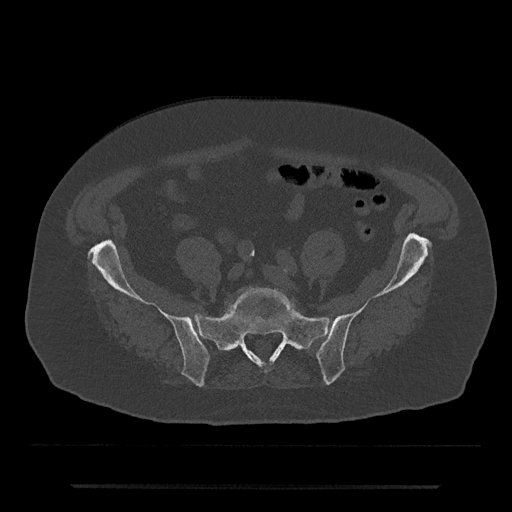
CT including the spine, one axial slice. Slice 246 of 797 in the series (ordered by position). Reconstruction kernel Br40s/3. 120 kVp. Bone window (W 1800 / L 400 HU). 512 × 512 image matrix, field of view 434 × 434 mm. Male patient, age 80 years. From the clinical record (not read from this slice): primary cancer: prostate.
Outlined on this slice (semi-automatic segmentation, software-assisted and operator-edited):
- L5 vertebra: bounding box [x1, y1, x2, y2] px = [228, 287, 299, 317]